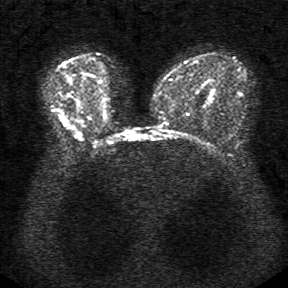
Breast MRI, one axial slice. Position 18 of 34 along the scan axis. Diffusion-weighted series; image 2 of 4 stored at this slice position (different b-values; order by instance number). 1.5 T. 5 mm slice thickness. 288 × 288 image matrix. Female patient.
Structures marked on this image (outlined manually by an expert reader):
- tumour on diffusion-weighted imaging: bounding box (x1, y1, x2, y2) in pixels: (61, 117, 64, 120)